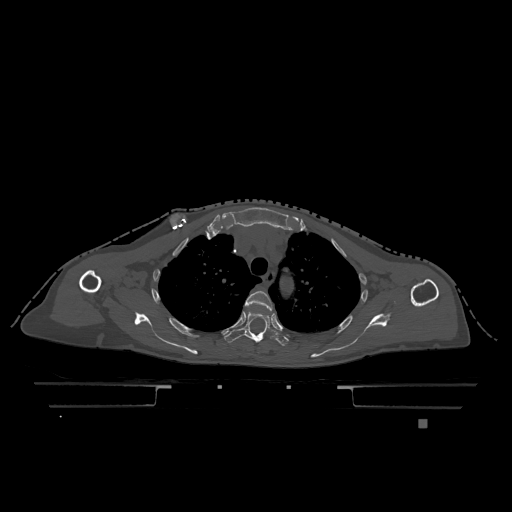
CT including the spine, one axial slice; slice 894 of 1317 in the series (ordered by position); bone window (W 1800 / L 400 HU); 0.5 mm slice thickness; 512 × 512 image matrix, field of view 500 × 500 mm. Patient: female, 74 years. From the clinical record (not read from this slice): primary cancer: lung; vertebrae with lytic lesions (as recorded): T1, T4, T5, T6, L4, L5.
Outlined on this slice (semi-automatic segmentation, software-assisted and operator-edited):
- T3 vertebra: bounding box (x1, y1, x2, y2) in pixels: (245, 290, 273, 311)
- T4 vertebra: (224, 307, 289, 346)